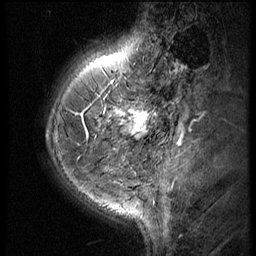
Breast MRI (dynamic contrast-enhanced), one sagittal slice; position 17 of 60 along the scan axis; 3 images stored at this slice position (order not interpretable as contrast timing); 1.5 T; TE 4.2 ms, TR 9 ms; 256 × 256 image matrix, field of view 180 × 180 mm. Female patient, age 38 years. Case-level facts recorded for this patient, not image findings: setting: breast cancer imaged before/during neoadjuvant chemotherapy; receptor status: triple-negative.
Structures marked on this image (semi-automatically segmented with operator editing):
- analysis volume of interest (the breast-tissue region the enhancement analysis was run in; not a lesion): bounding box <119,93,165,150> (left, top, right, bottom; pixels)
- tumour enhancement mask (voxels above the 140 % enhancement threshold inside the analysis volume of interest): <119,110,149,135>